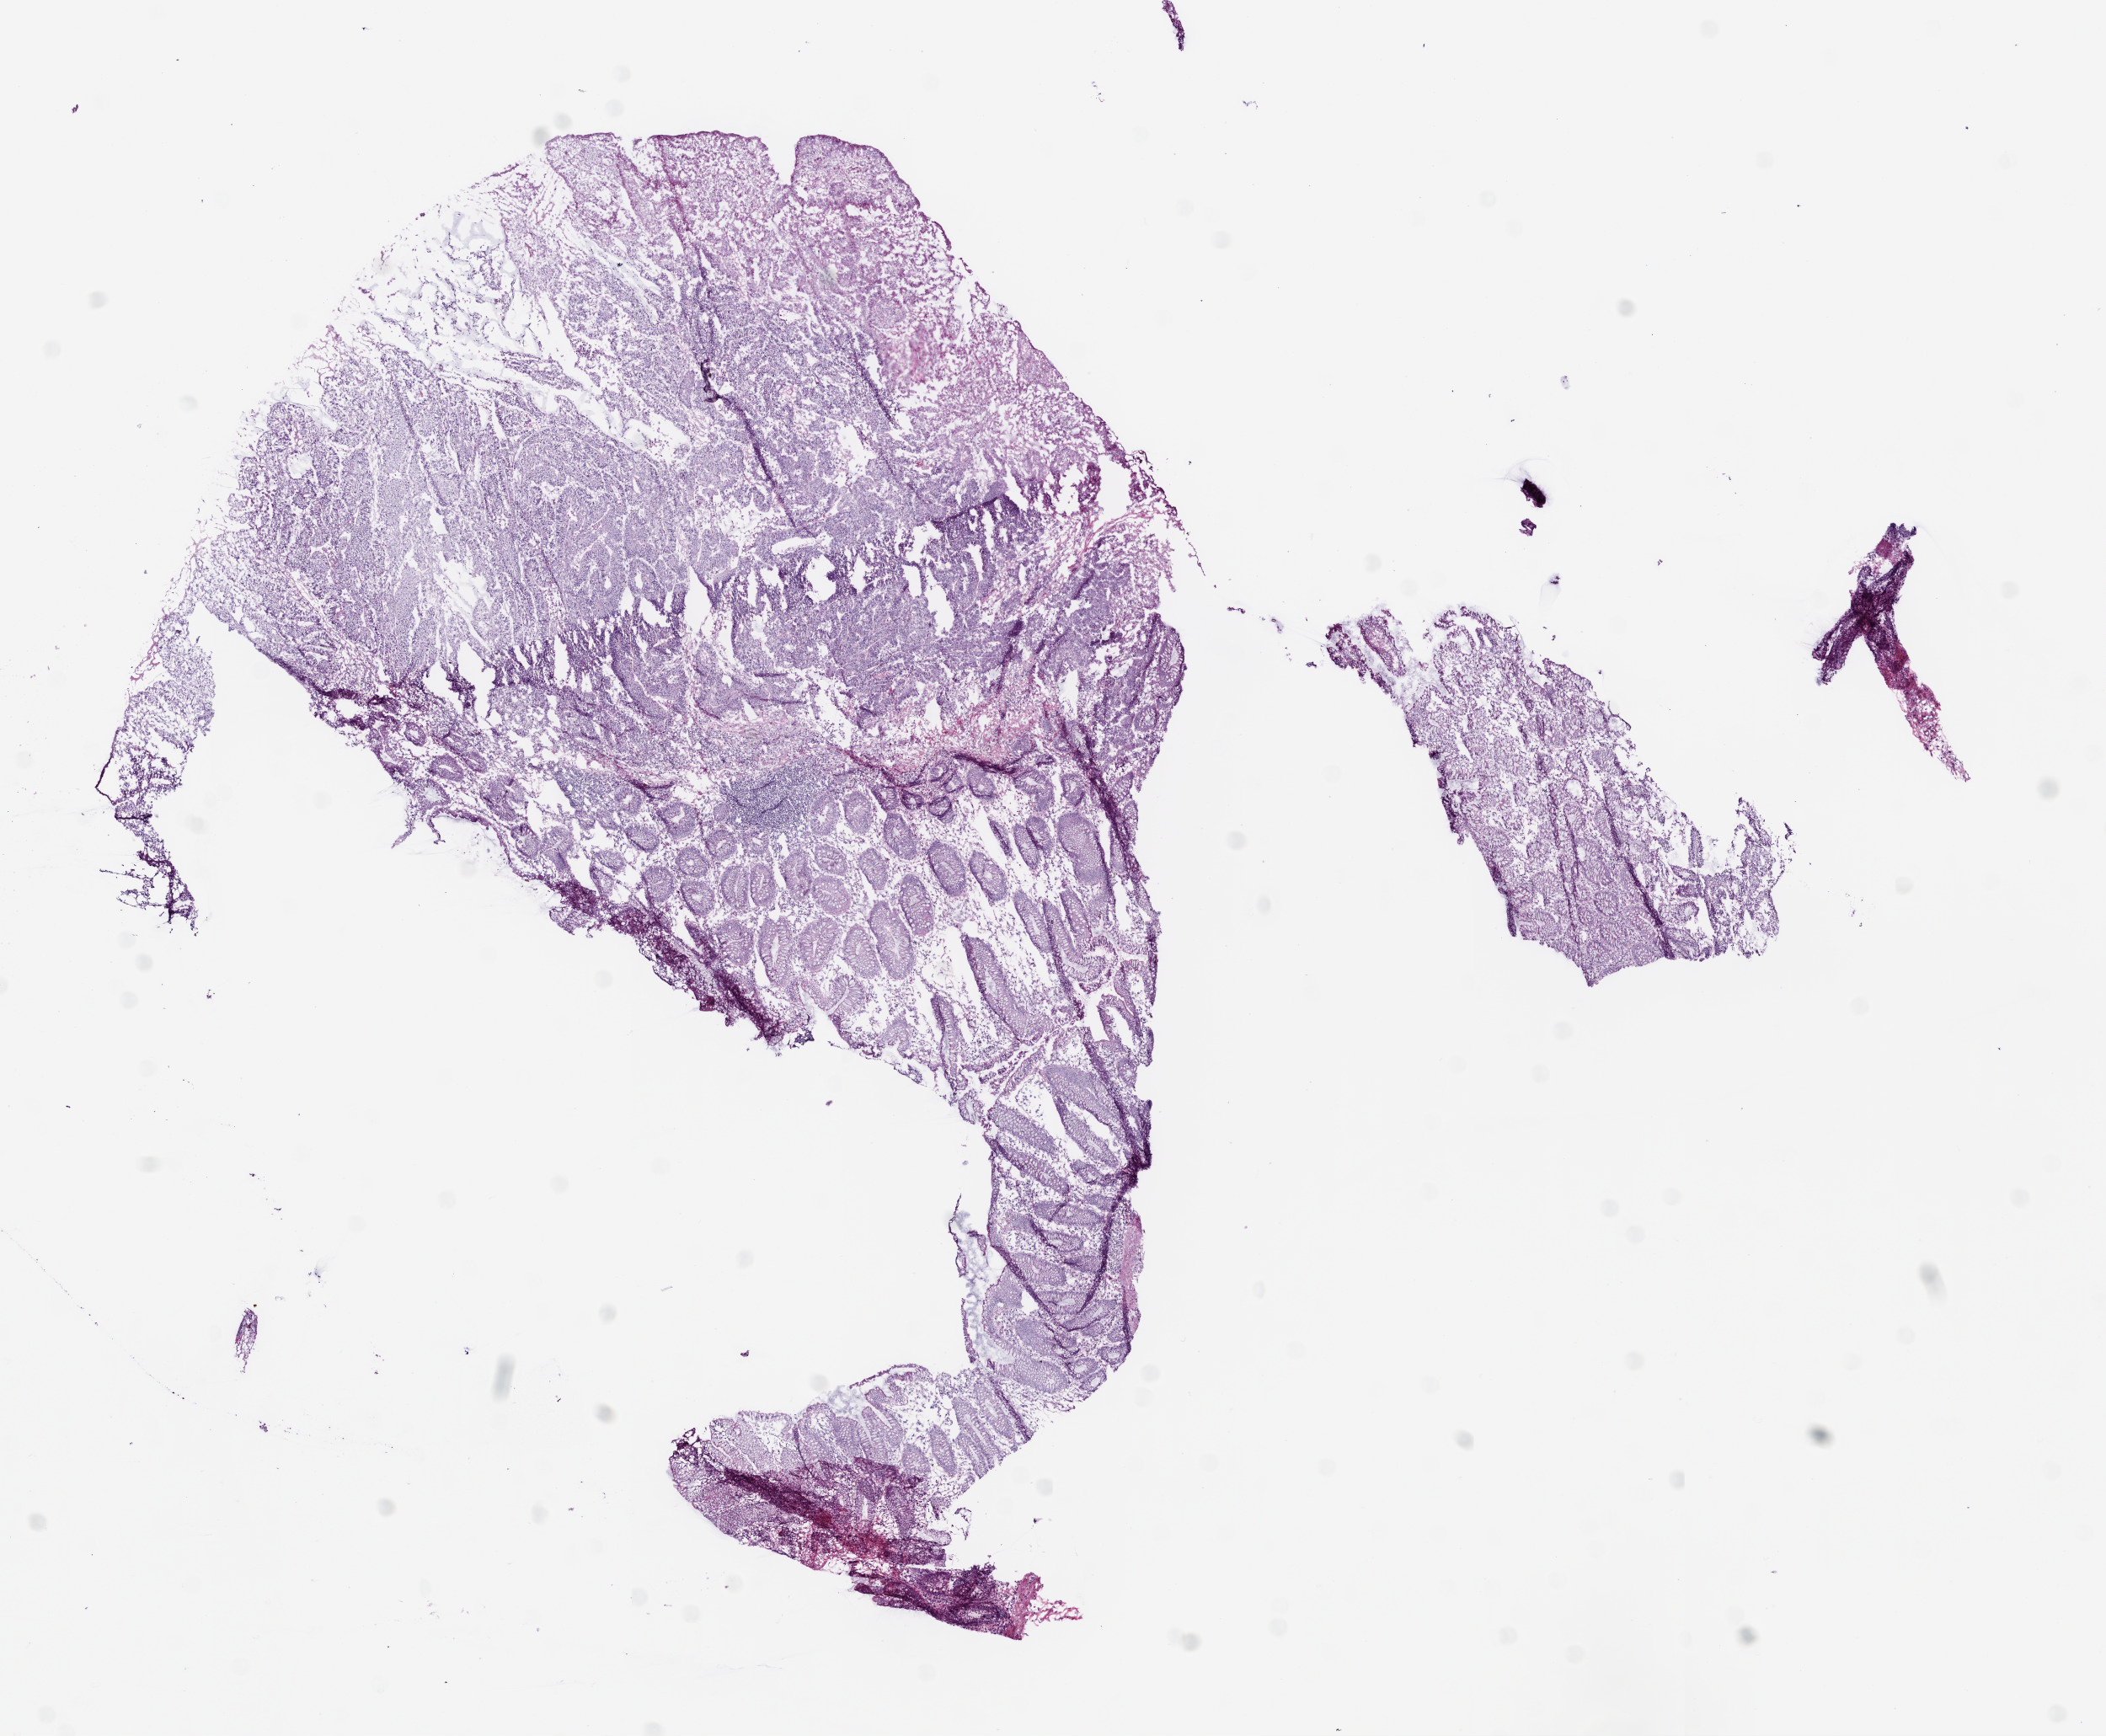
H&E-stained whole-slide image — low-resolution overview of the scanned area, about 10.0 x 8.3 mm. Frozen section from the bottom of the tissue portion. Sample: primary tumour, colon. Patient: male, age at initial diagnosis 68 years. Pathologist review of this section (percent, as recorded): tumour cells 55%, tumour nuclei 73%, normal cells 44%, necrosis 1%. Infiltration values recorded for this section: lymphocyte infiltration 1%.
AJCC pathologic stage: IV (5th edition). Lymph nodes positive (case pathology): 0 of 15 examined. Histologic diagnosis: Adenocarcinoma, NOS.